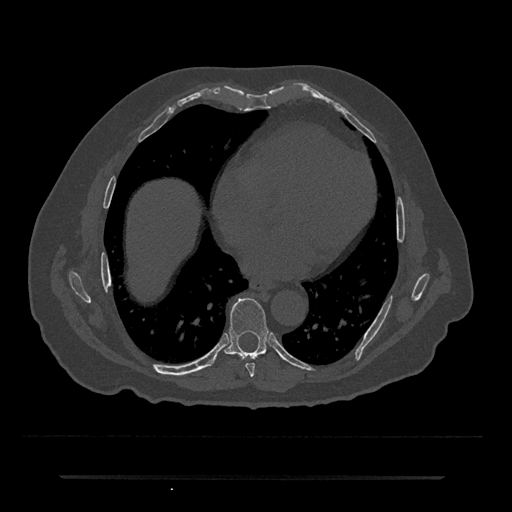
CT including the spine, one axial slice; slice 350 of 797 in the series (ordered by position); 120 kVp; bone window (W 1800 / L 400 HU); 0.5 mm slice thickness; 512 × 512 image matrix, field of view 437 × 437 mm. Patient: male, 69 years. Case-level facts recorded for this patient, not image findings: primary cancer: prostate.
Structures marked on this image (semi-automatically segmented with operator editing):
- T7 vertebra: box from (x=245, y=363) to (x=255, y=377) px
- T8 vertebra: (x=224, y=298)–(x=268, y=360)